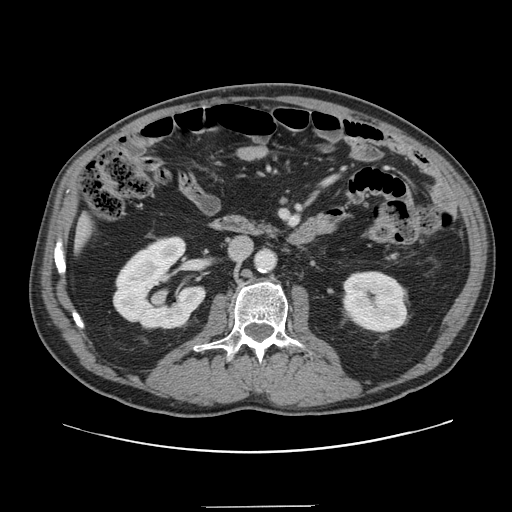
Contrast-enhanced abdominal CT, one axial slice. Position 51 of 139 along the scan axis. Intravenous contrast given. Soft-tissue window (W 400 / L 40 HU). 2.5 mm slice thickness. 512 × 512 image matrix, field of view 397 × 397 mm. Male patient, age 64 years. Case-level facts recorded for this patient, not image findings: diagnosis: colorectal cancer liver metastases, imaged before liver resection; multiple liver metastases: yes; largest metastasis: 3.5 cm; disease in both lobes: yes.
Annotated regions visible in this slice (manually delineated by an expert):
- liver: bounding box (x1, y1, x2, y2) in pixels: (80, 219, 89, 239)
- planned liver remnant (the part of the liver to remain after resection): (79, 220, 89, 243)